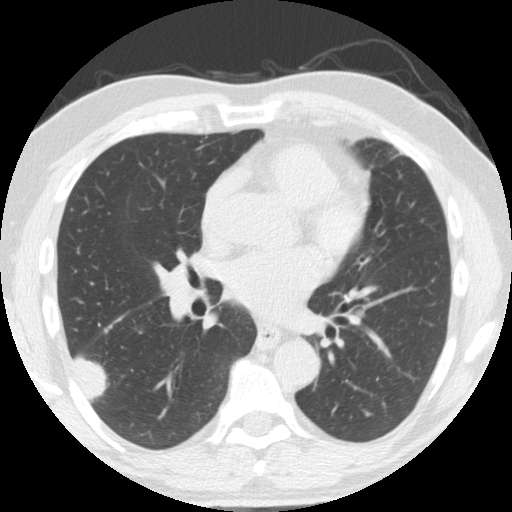
Low-dose screening chest CT, one axial slice; slice 84 of 174 in the series (ordered by position); reconstruction kernel STANDARD; 120 kVp; lung window (W 1500 / L -600 HU); 2.5 mm slice thickness; 512 × 512 image matrix, field of view 341 × 341 mm.
Structures marked on this image (manually delineated by an expert):
- lesion 1 (tumor, lower lobe of right lung): bounding box <73,356,108,400> (left, top, right, bottom; pixels)